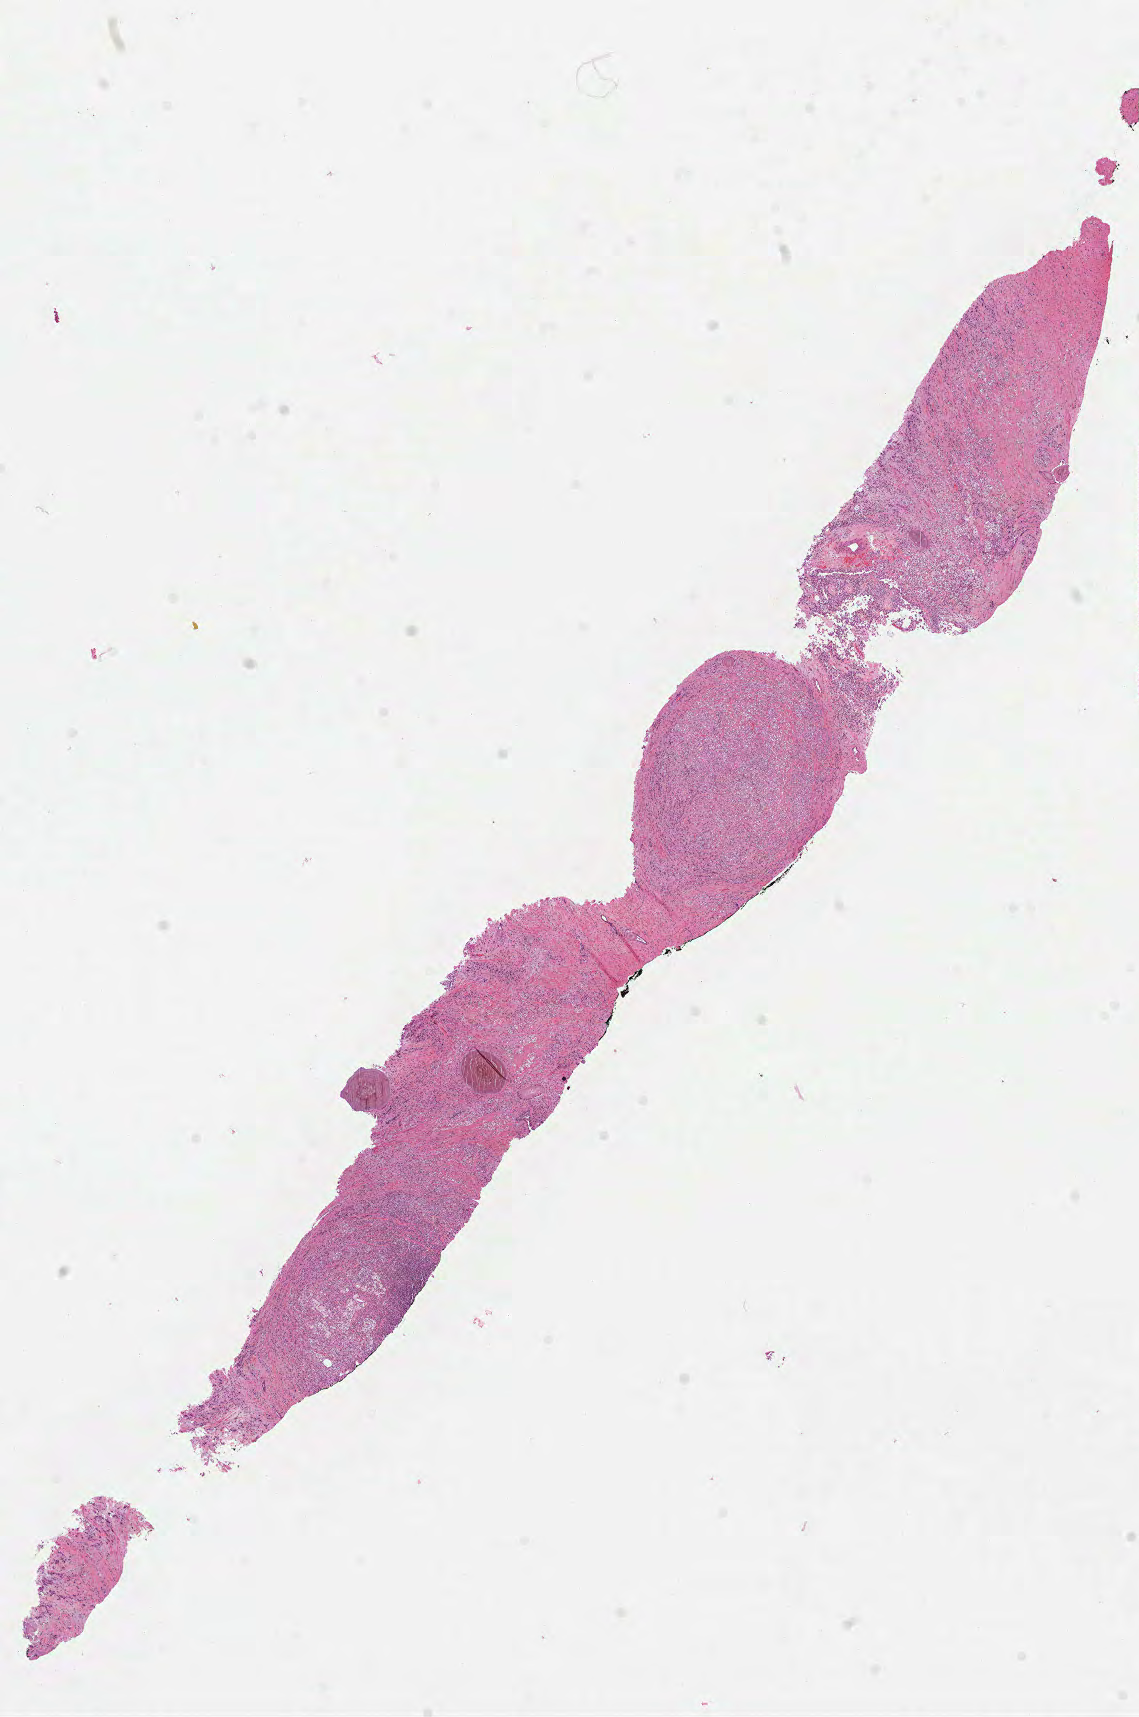
Whole-slide histology image, Hematoxylin and eosin (H&E) stained — low-resolution overview of the scanned area, about 9.2 x 13.8 mm, formalin-fixed paraffin-embedded (FFPE) diagnostic section, prostate, primary tumour sample. Male patient; age at initial diagnosis 56 years. Gleason score: 9 (5+4).
* laterality: bilateral
* pathologic diagnosis: Adenocarcinoma, NOS (prostate gland)
* lymph nodes positive (case pathology): 0 of 13 examined